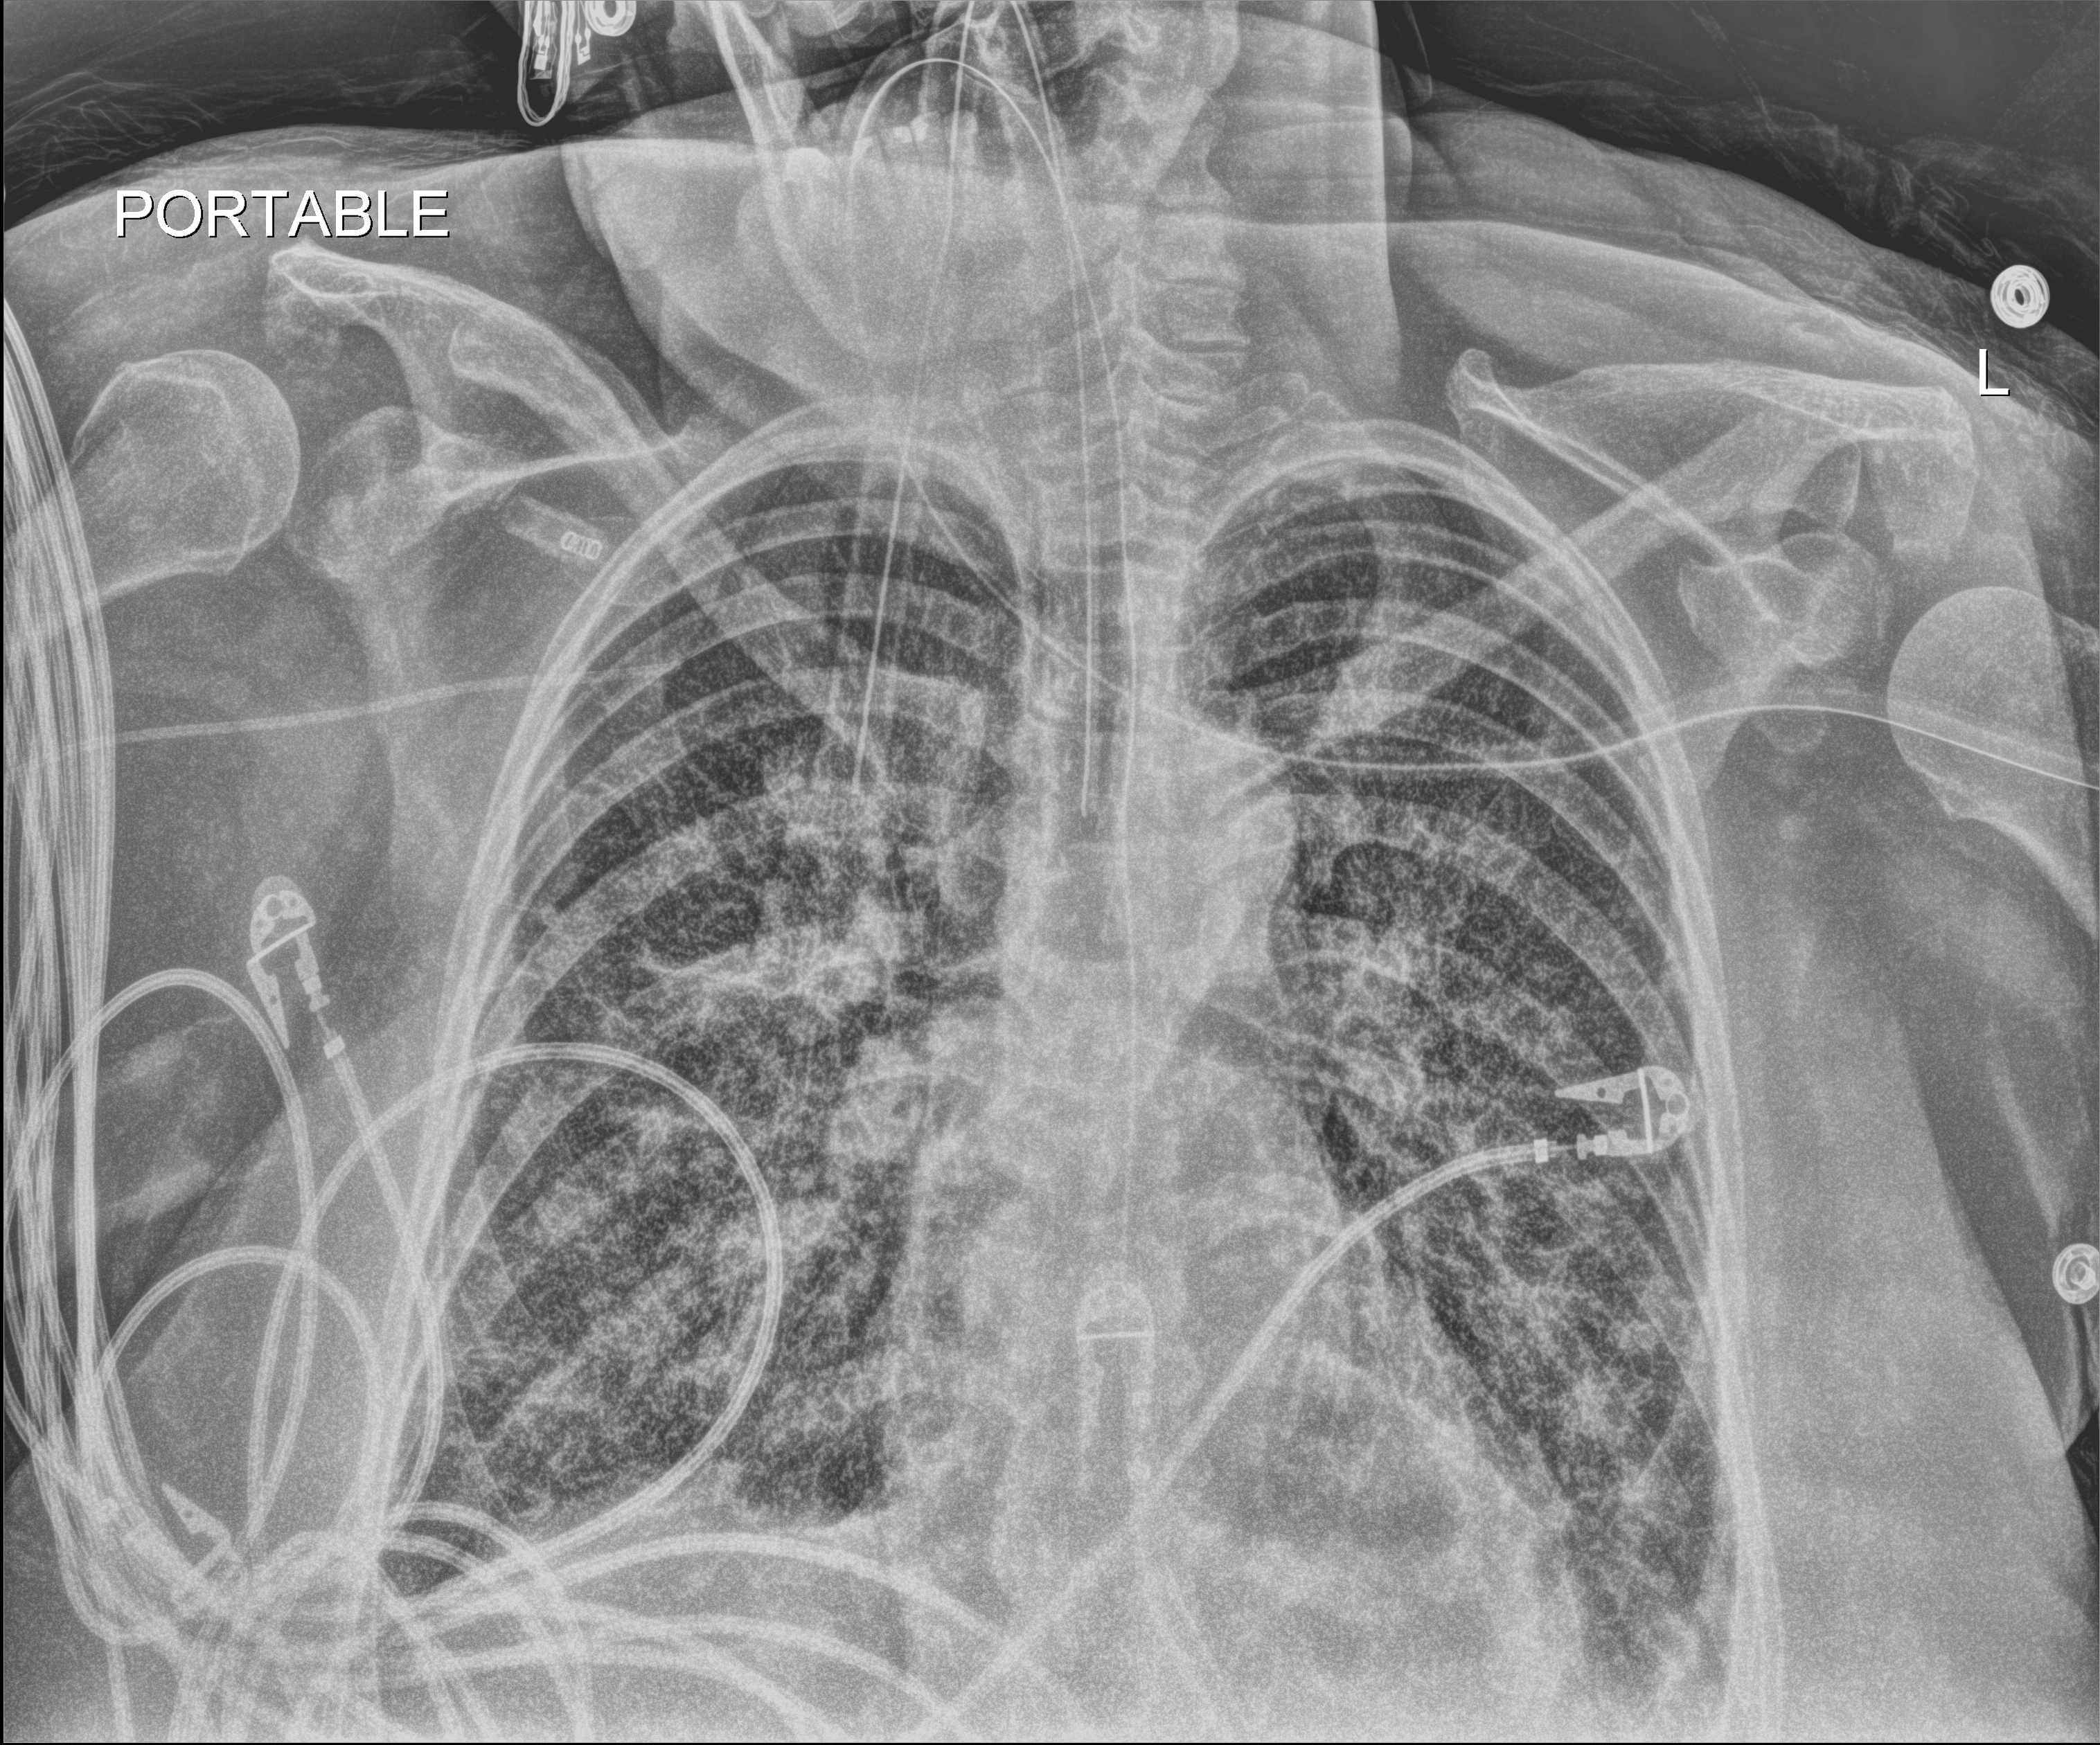
Chest X-ray (portable); anteroposterior (AP) projection. Female patient hospitalised with COVID-19, age 60–74 years.
From the hospital-stay record, not from the radiograph (when in the stay this image was taken is not recorded): hypertension (admission record): no; mechanically ventilated during this hospital stay: yes.